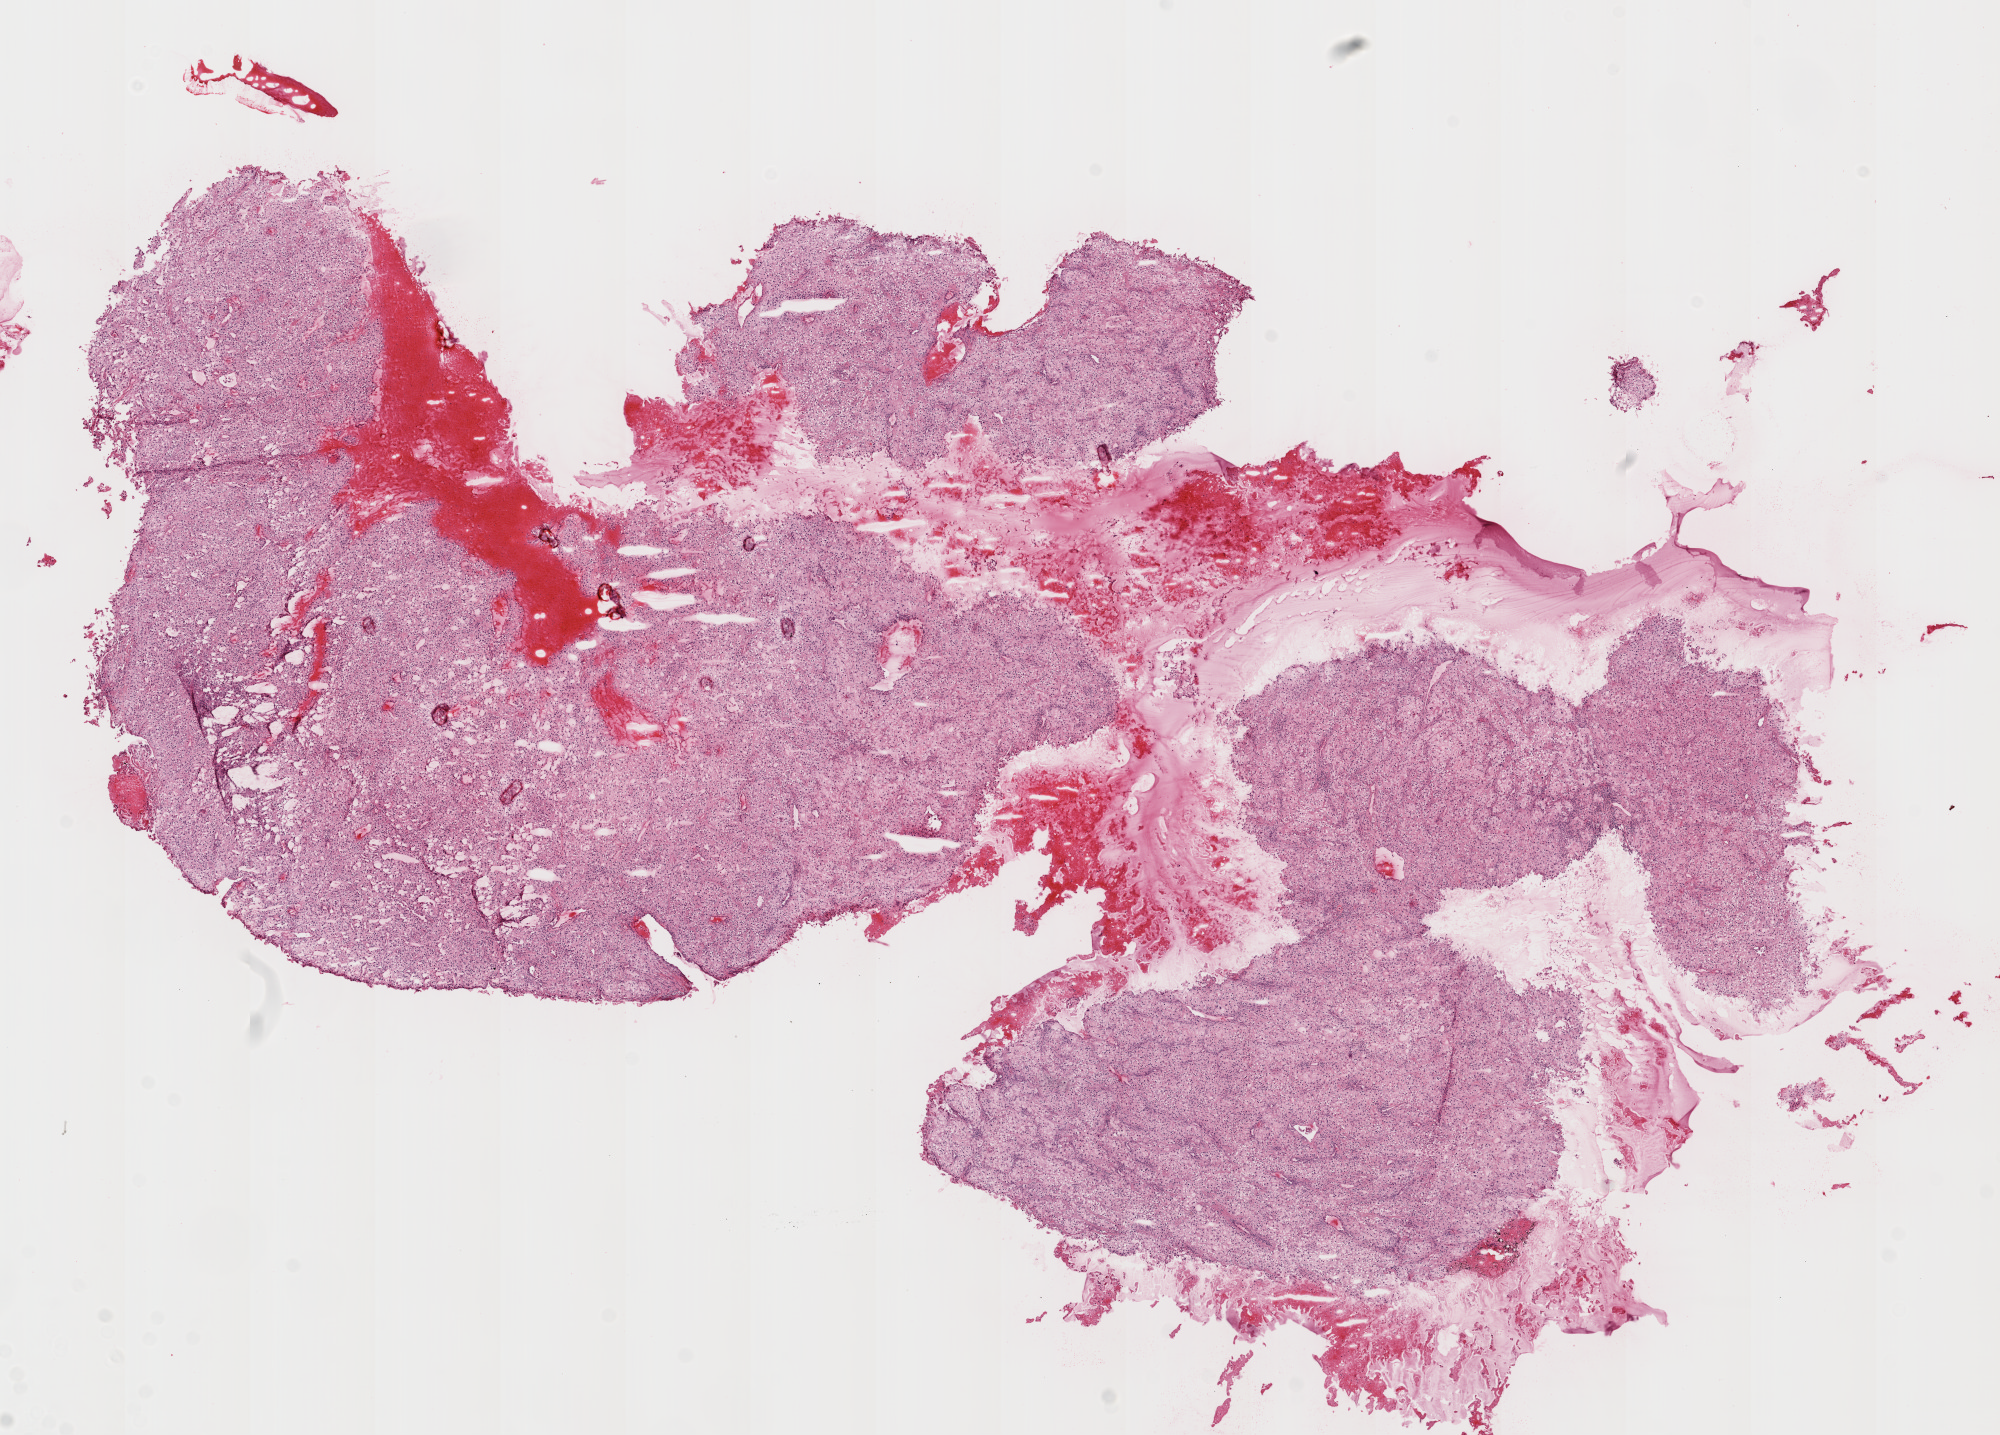
Hematoxylin and eosin (H&E) stained whole-slide image — whole scanned area (about 16.0 x 11.5 mm) shown as a low-resolution overview, frozen section from the top of the tissue portion, kidney, primary tumour sample. Patient: male, age at initial diagnosis 57 years. Histologic grade: G3 (poorly differentiated). Pathologist review of this section (percent, as recorded): tumour cells 85%, tumour nuclei 90%, normal cells 0%, stromal cells 15%, necrosis 0%. Infiltration values recorded for this section: lymphocyte infiltration 2%, monocyte infiltration 2%, neutrophil infiltration 0%.
Lymph nodes positive (case pathology): 0 of 7 examined. AJCC pathologic stage: II (6th edition). Diagnosis: Clear cell adenocarcinoma, NOS. Laterality: left.